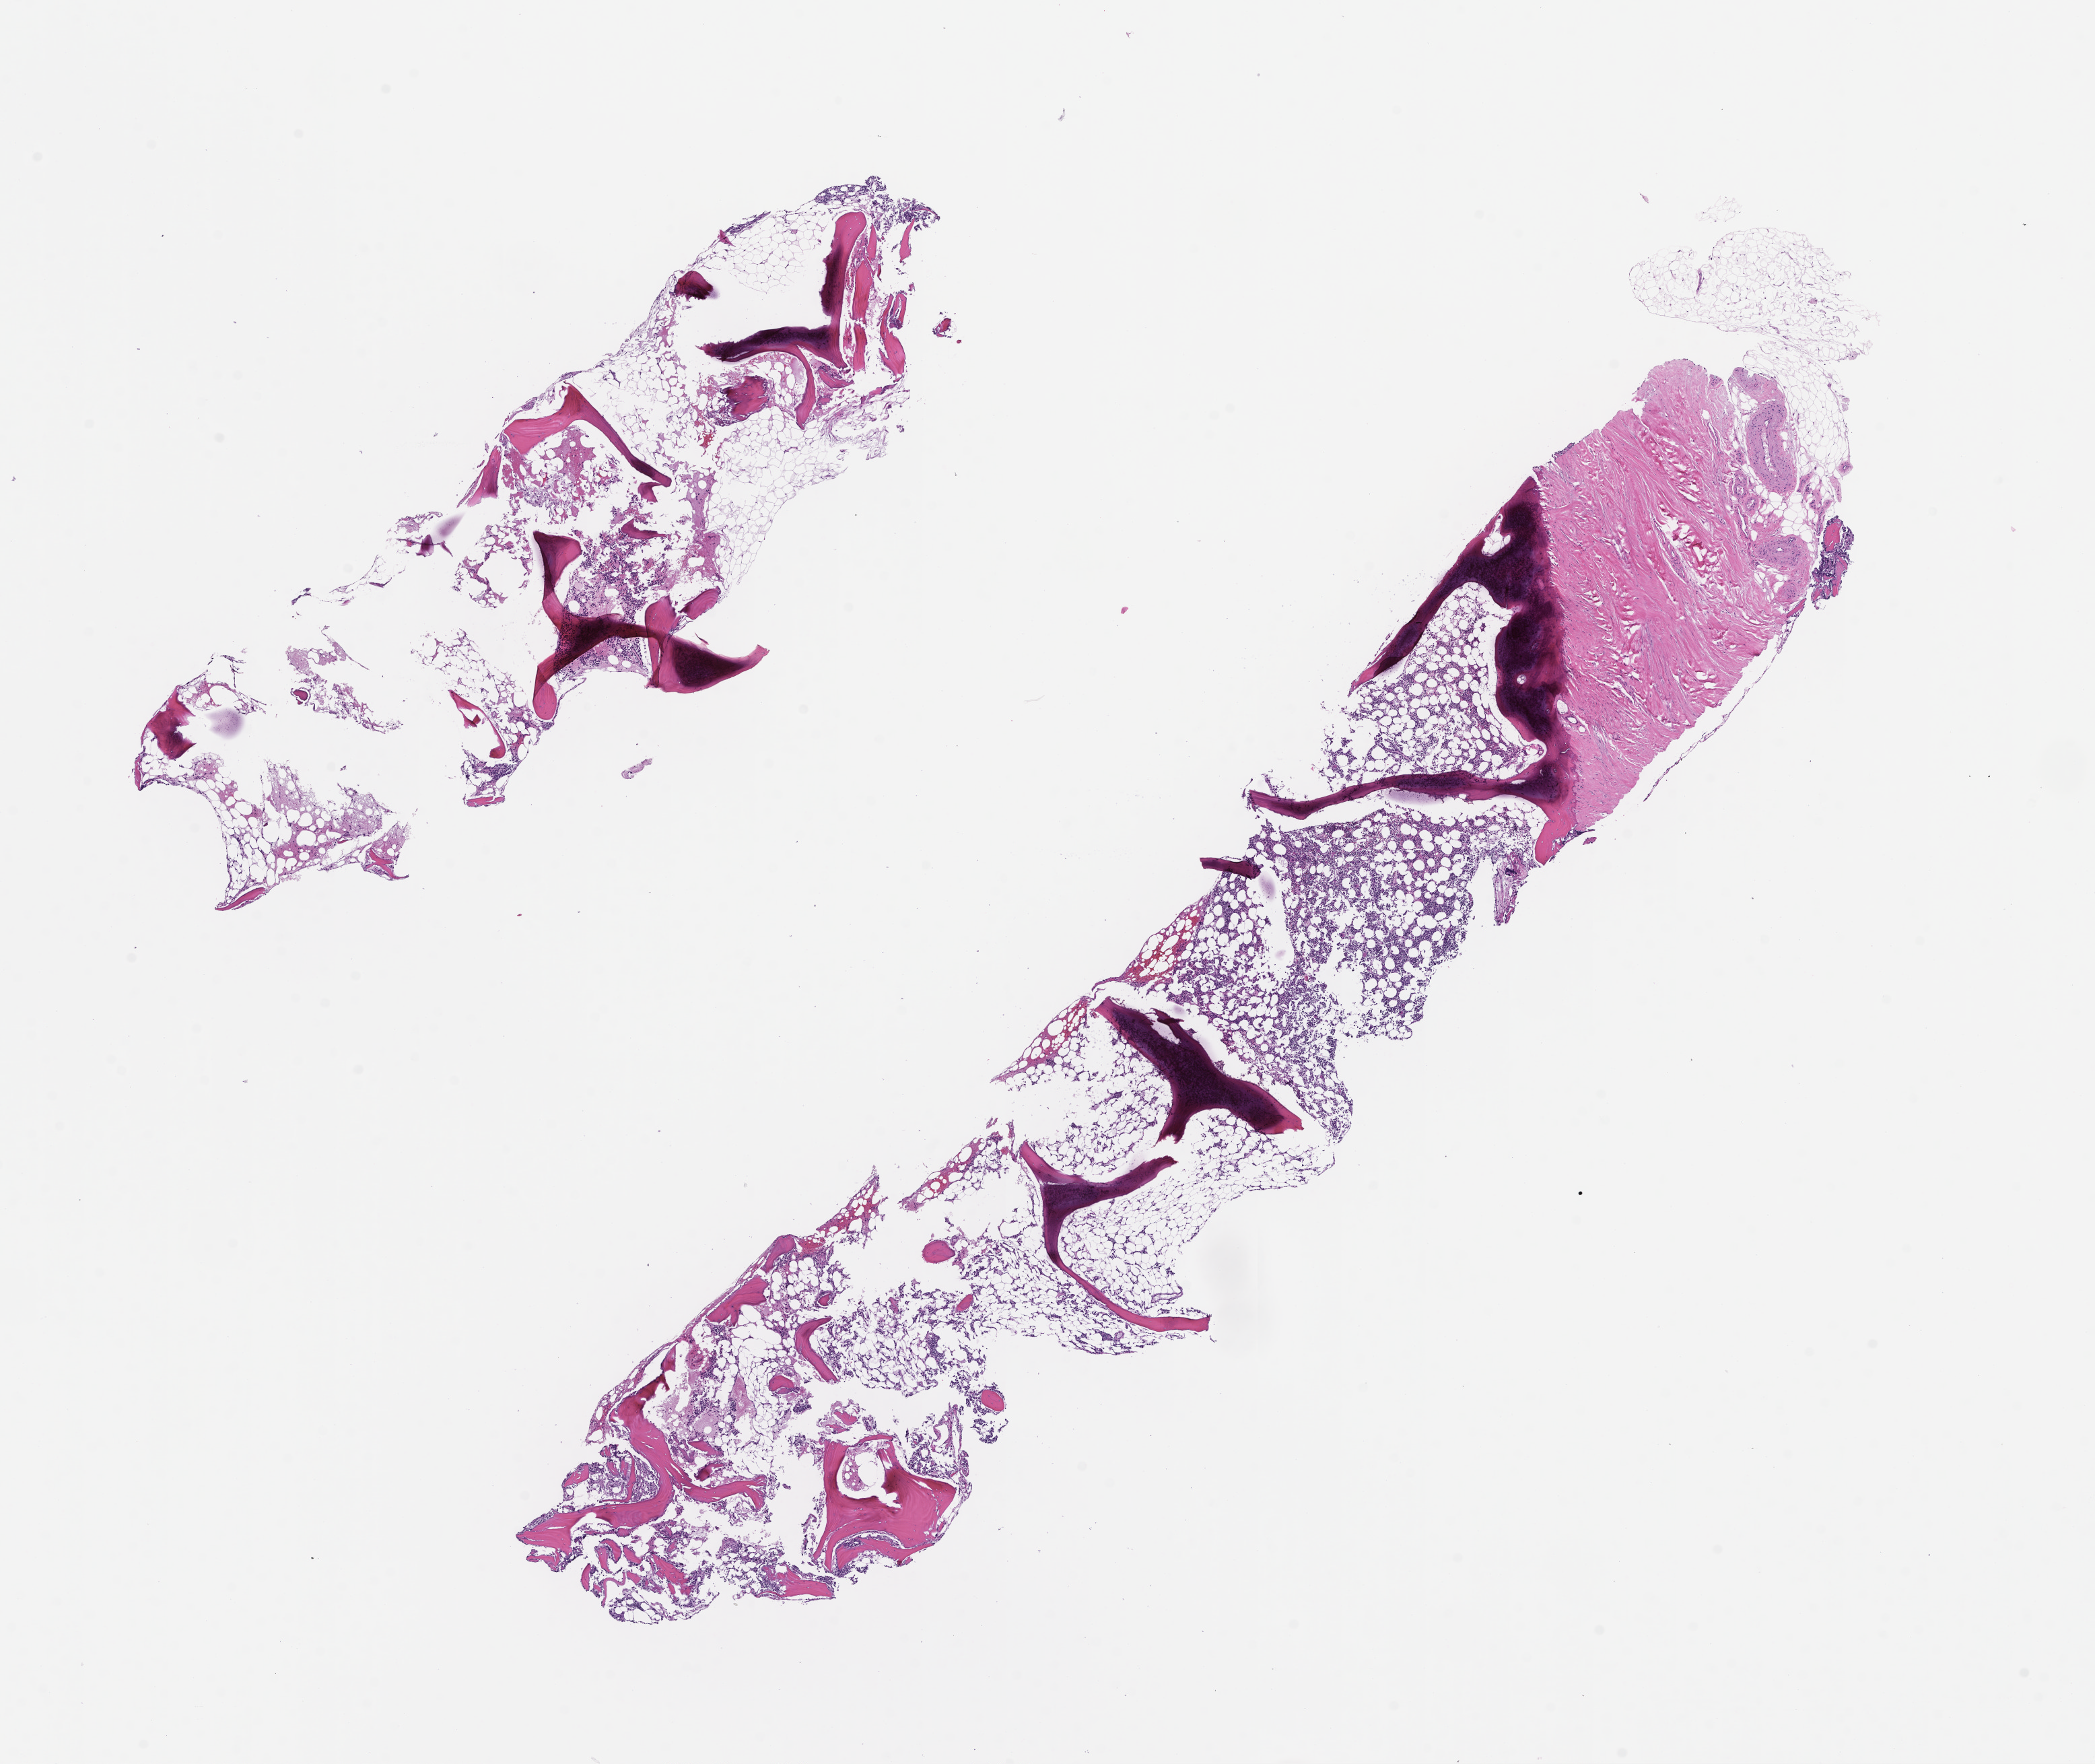
Digitized H&E-stained section — a low-resolution overview of the entire scanned area, about 12.6 x 10.6 mm, formalin-fixed, paraffin-embedded (FFPE) tissue. Patient sex: female.
- this section: metastatic tumor tissue
- primary diagnosis of the patient: Plasma Cell Myeloma